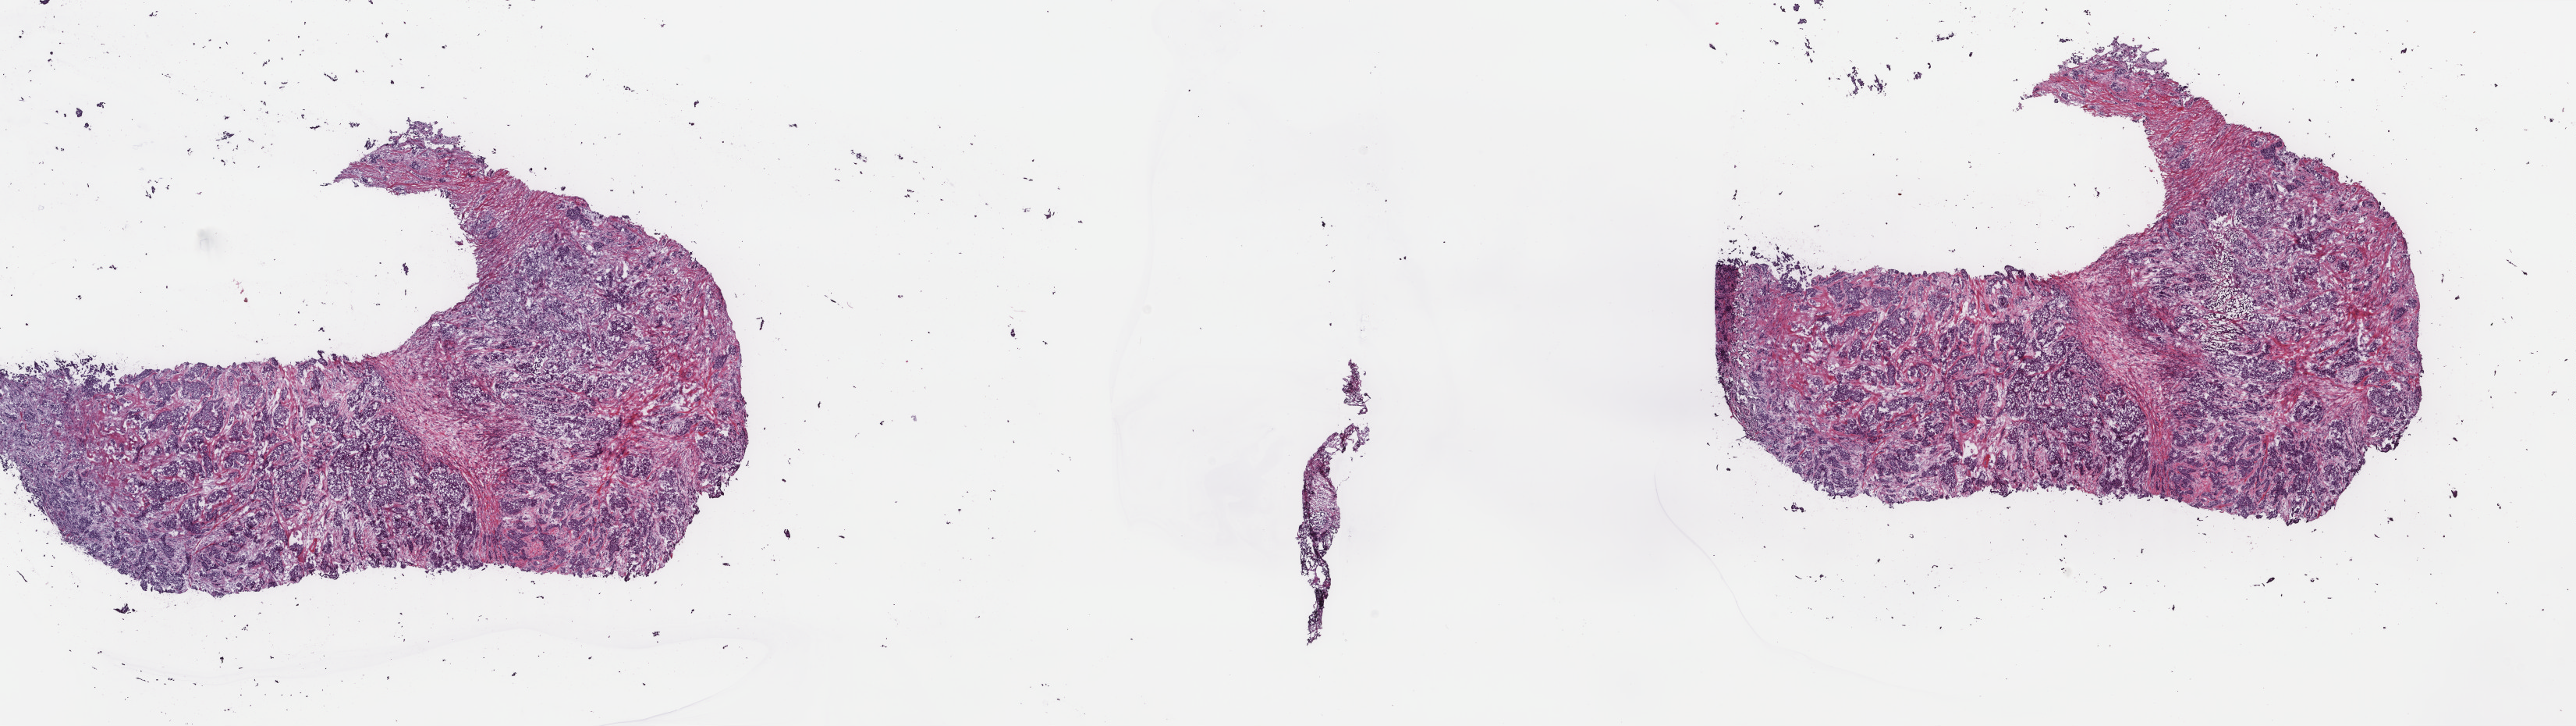
Digitized H&E tissue section (whole slide), whole scanned area (about 26.2 x 7.4 mm, from a 40x scan) shown as a low-resolution overview. Frozen section from the top of the tissue portion. Primary tumour sample from the breast. Patient sex: female. Pathologist review of this section (percent, as recorded): tumour cells 75%, tumour nuclei 85%, normal cells 0%, stromal cells 25%, necrosis 0%. Inflammatory infiltration, as recorded: lymphocyte infiltration 1%, monocyte infiltration 0%, neutrophil infiltration 0%.
- AJCC pathologic stage: IIA (7th edition)
- laterality: right
- pathologic diagnosis: Infiltrating duct carcinoma, NOS